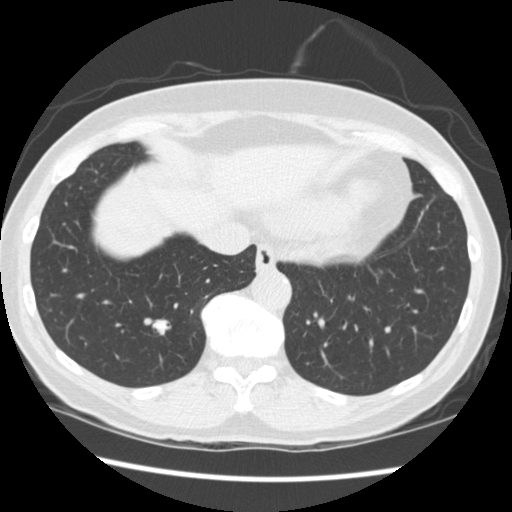
Low-dose screening chest CT, one axial slice; slice 69 of 262 in the series (ordered by position); reconstruction kernel STANDARD; lung window (W 1500 / L -600 HU); 2.5 mm slice thickness; 512 × 512 image matrix.
Annotated regions visible in this slice (expert manual segmentation):
- lesion 1 (tumor, lower lobe of right lung): bounding box [x1, y1, x2, y2] px = [153, 320, 170, 335]